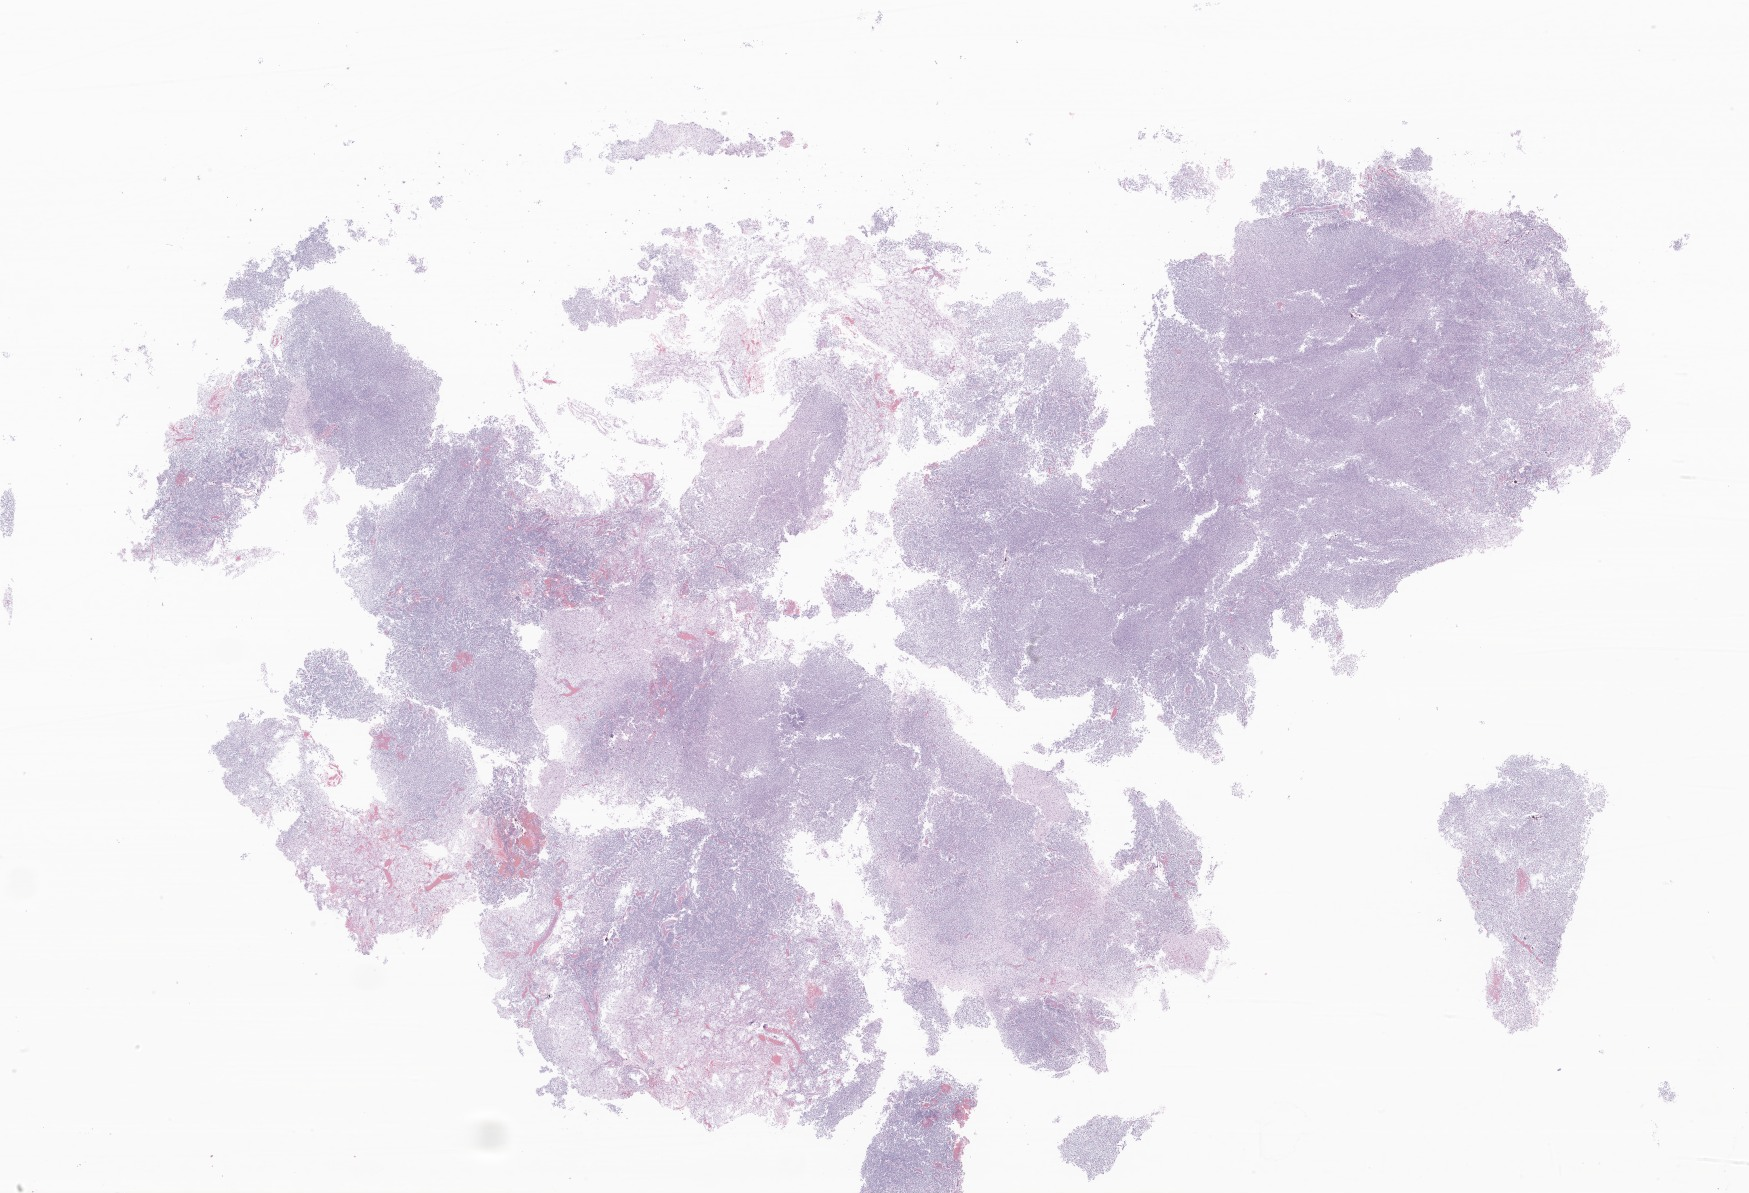
Hematoxylin and eosin (H&E) whole-slide image of tumor tissue from the temporal lobe — low-resolution overview of the scanned area, about 29.5 x 20.1 mm; formalin-fixed, paraffin-embedded (FFPE) tissue. Patient male; age 135 months (11 years 3 months).
- recorded diagnosis: Glioma, malignant